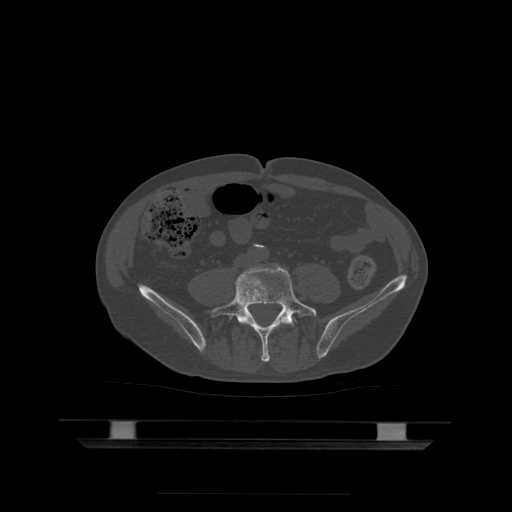
CT including the spine, one axial slice; position 76 of 522 along the scan axis; bone window (W 1800 / L 400 HU); 1.25 mm slice thickness; 512 × 512 image matrix, field of view 436 × 436 mm. Patient age 68 years. From the clinical record (not read from this slice): primary cancer: urothelial.
Structures marked on this image (semi-automatic segmentation, software-assisted and operator-edited):
- L4 vertebra: bounding box [x1, y1, x2, y2] px = [288, 322, 291, 324]
- L5 vertebra: [211, 267, 317, 362]